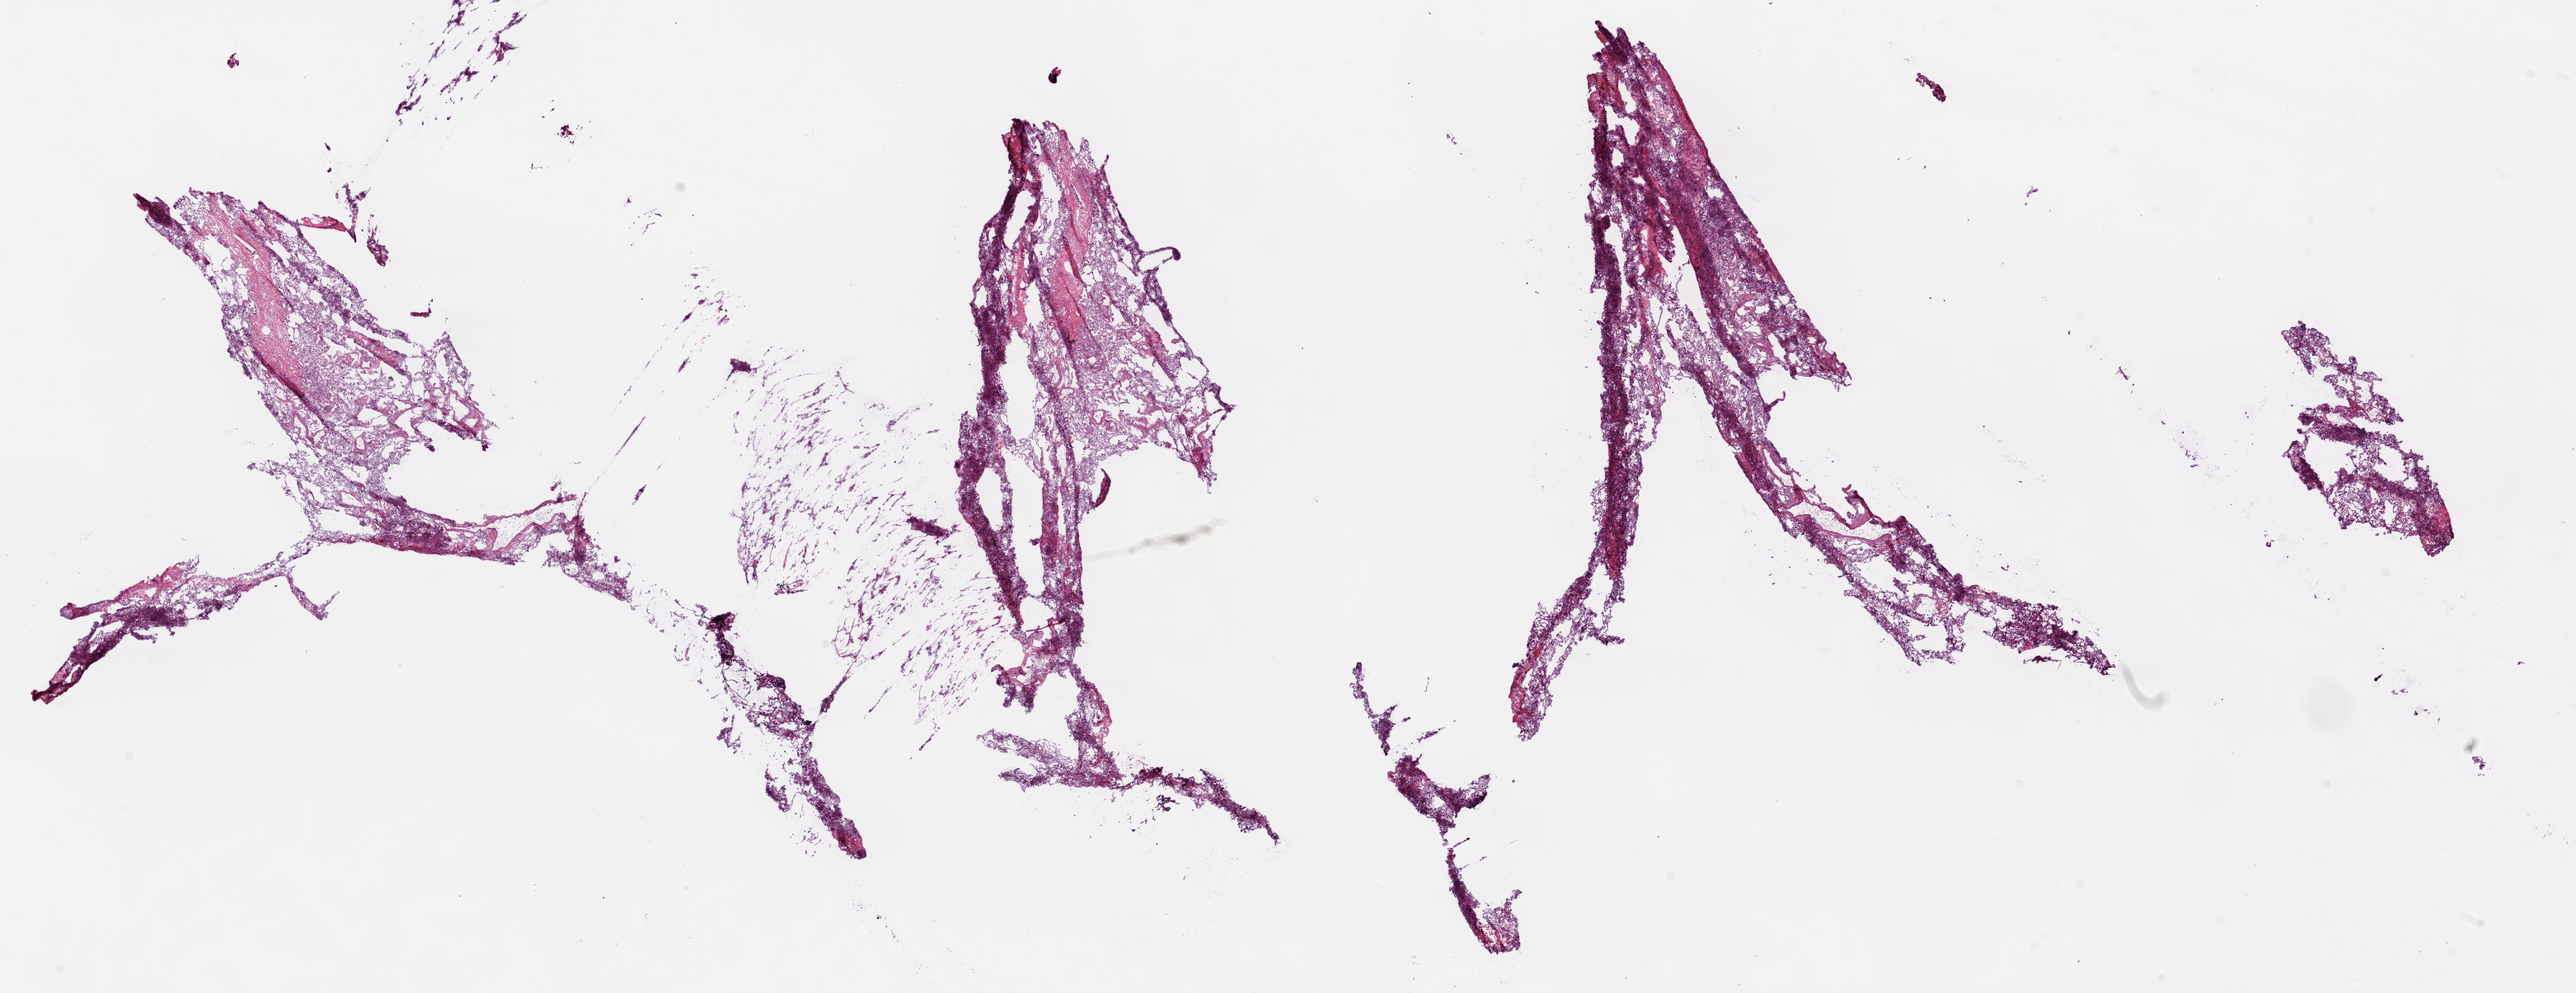
Whole-slide histology image, Hematoxylin and eosin (H&E) stained — whole scanned area (about 25.1 x 9.7 mm) shown as a low-resolution overview; frozen section from the bottom of the tissue portion; sample: solid tissue normal (non-tumour tissue), lung. Male patient; age at initial diagnosis 51 years.
This section: solid tissue normal (non-tumour) sample from the same patient. Patient diagnosis: Squamous cell carcinoma, NOS (upper lobe, lung).